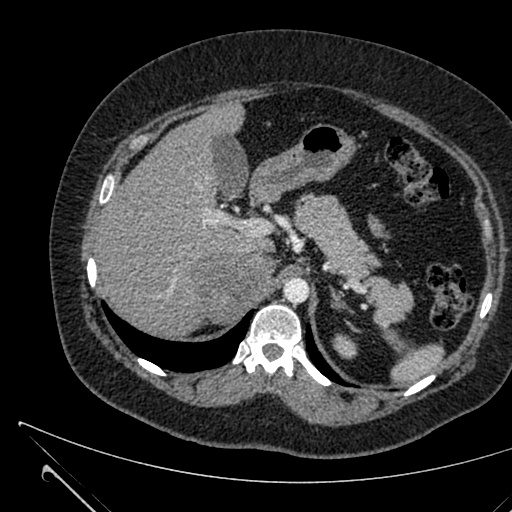
Contrast-enhanced abdominal CT, one axial slice; slice 460 of 731 in the series (ordered by position); intravenous contrast given; soft-tissue window (W 400 / L 40 HU); 1 mm slice thickness; 512 × 512 image matrix, field of view 376 × 376 mm. Patient: female, 36 years. Case-level facts recorded for this patient, not image findings: diagnosis: adrenocortical carcinoma; tumour side: right adrenal; tumour size at pathology: 10 cm; Ki-67 index: 20 %; stage (as recorded): 4.
Outlined on this slice (semi-automatic segmentation, software-assisted and operator-edited):
- mass: box from (x=194, y=254) to (x=274, y=321) px